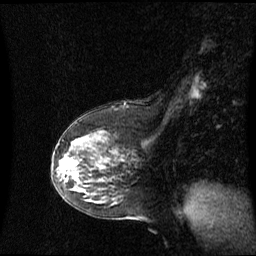
Breast MRI (dynamic contrast-enhanced), one sagittal slice. Slice 35 of 60 in the series (ordered by position). Dynamic contrast-enhanced series, image 2 of 3 at this slice position (ordered by acquisition). 1.5 T. TE 4.2 ms, TR 8.4 ms. 2.1 mm slice thickness. 256 × 256 image matrix, field of view 260 × 260 mm. Patient: female, 59 years. Case-level facts recorded for this patient, not image findings: setting: breast cancer imaged before/during neoadjuvant chemotherapy; receptor status: HR-positive, HER2-negative.
Structures marked on this image (semi-automatically segmented with operator editing):
- analysis volume of interest (the breast-tissue region the enhancement analysis was run in; not a lesion): bounding box [x1, y1, x2, y2] px = [58, 153, 85, 191]
- tumour enhancement mask (voxels above the 70 % enhancement threshold inside the analysis volume of interest): [67, 163, 77, 177]